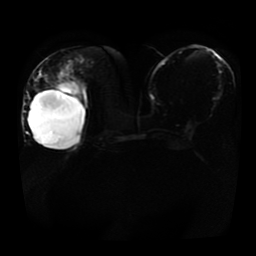
Breast MRI, one axial slice; diffusion-weighted series; image 2 of 4 stored at this slice position (different b-values; order by instance number); 1.5 T; 256 × 256 image matrix, field of view 360 × 360 mm. Female patient.
Annotated regions visible in this slice (expert manual segmentation):
- tumour on diffusion-weighted imaging: box from (x=54, y=79) to (x=84, y=104) px